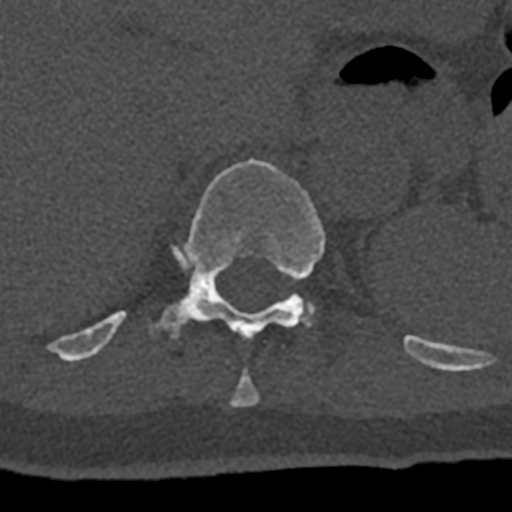
CT including the spine, one axial slice; 120 kVp; bone window (W 1800 / L 400 HU); 0.5 mm slice thickness; 512 × 512 image matrix, field of view 160 × 160 mm. Male patient, age 74 years. From the clinical record (not read from this slice): primary cancer: renal; vertebrae with lytic lesions (as recorded): T10, L1, L2, L3, L4, L5.
Annotated regions visible in this slice (semi-automatically segmented with operator editing):
- T10 vertebra: bounding box [x1, y1, x2, y2] px = [232, 370, 259, 407]
- T11 vertebra: [70, 158, 432, 367]
- T12 vertebra: [303, 302, 315, 323]